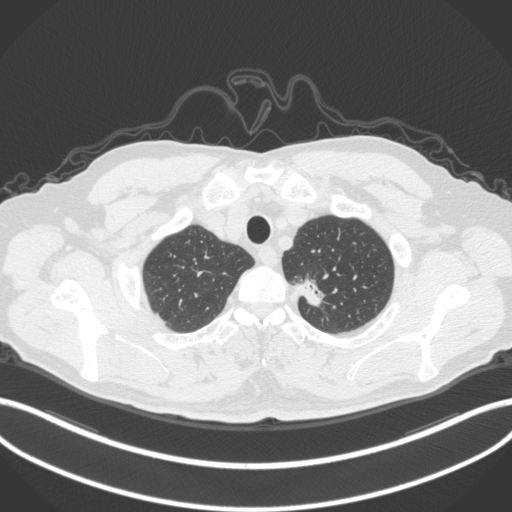
Chest CT, one axial slice; slice 336 of 382 in the series (ordered by position); reconstruction kernel B31f; 120 kVp; lung window (W 1500 / L -600 HU); 1 mm slice thickness; 512 × 512 image matrix, field of view 400 × 400 mm. Patient: male, 64 years. From the clinical record (not read from this slice): clinical TNM (as recorded): T1c N0 M0.
Annotated regions visible in this slice (rectangle marked by the reading radiologist):
- lung tumour (recorded histology: adenocarcinoma): bounding box <296,273,330,311> (left, top, right, bottom; pixels)